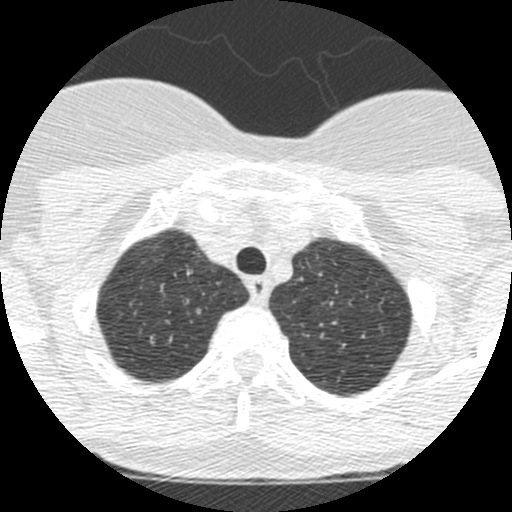
Low-dose screening chest CT, one axial slice. Position 209 of 250 along the scan axis. 120 kVp. Lung window (W 1500 / L -600 HU). 1.25 mm slice thickness. 512 × 512 image matrix, field of view 257 × 257 mm.
Annotated regions visible in this slice (expert manual segmentation):
- lesion 1 (tumor, upper lobe of right lung): bounding box [x1, y1, x2, y2] px = [197, 309, 201, 314]